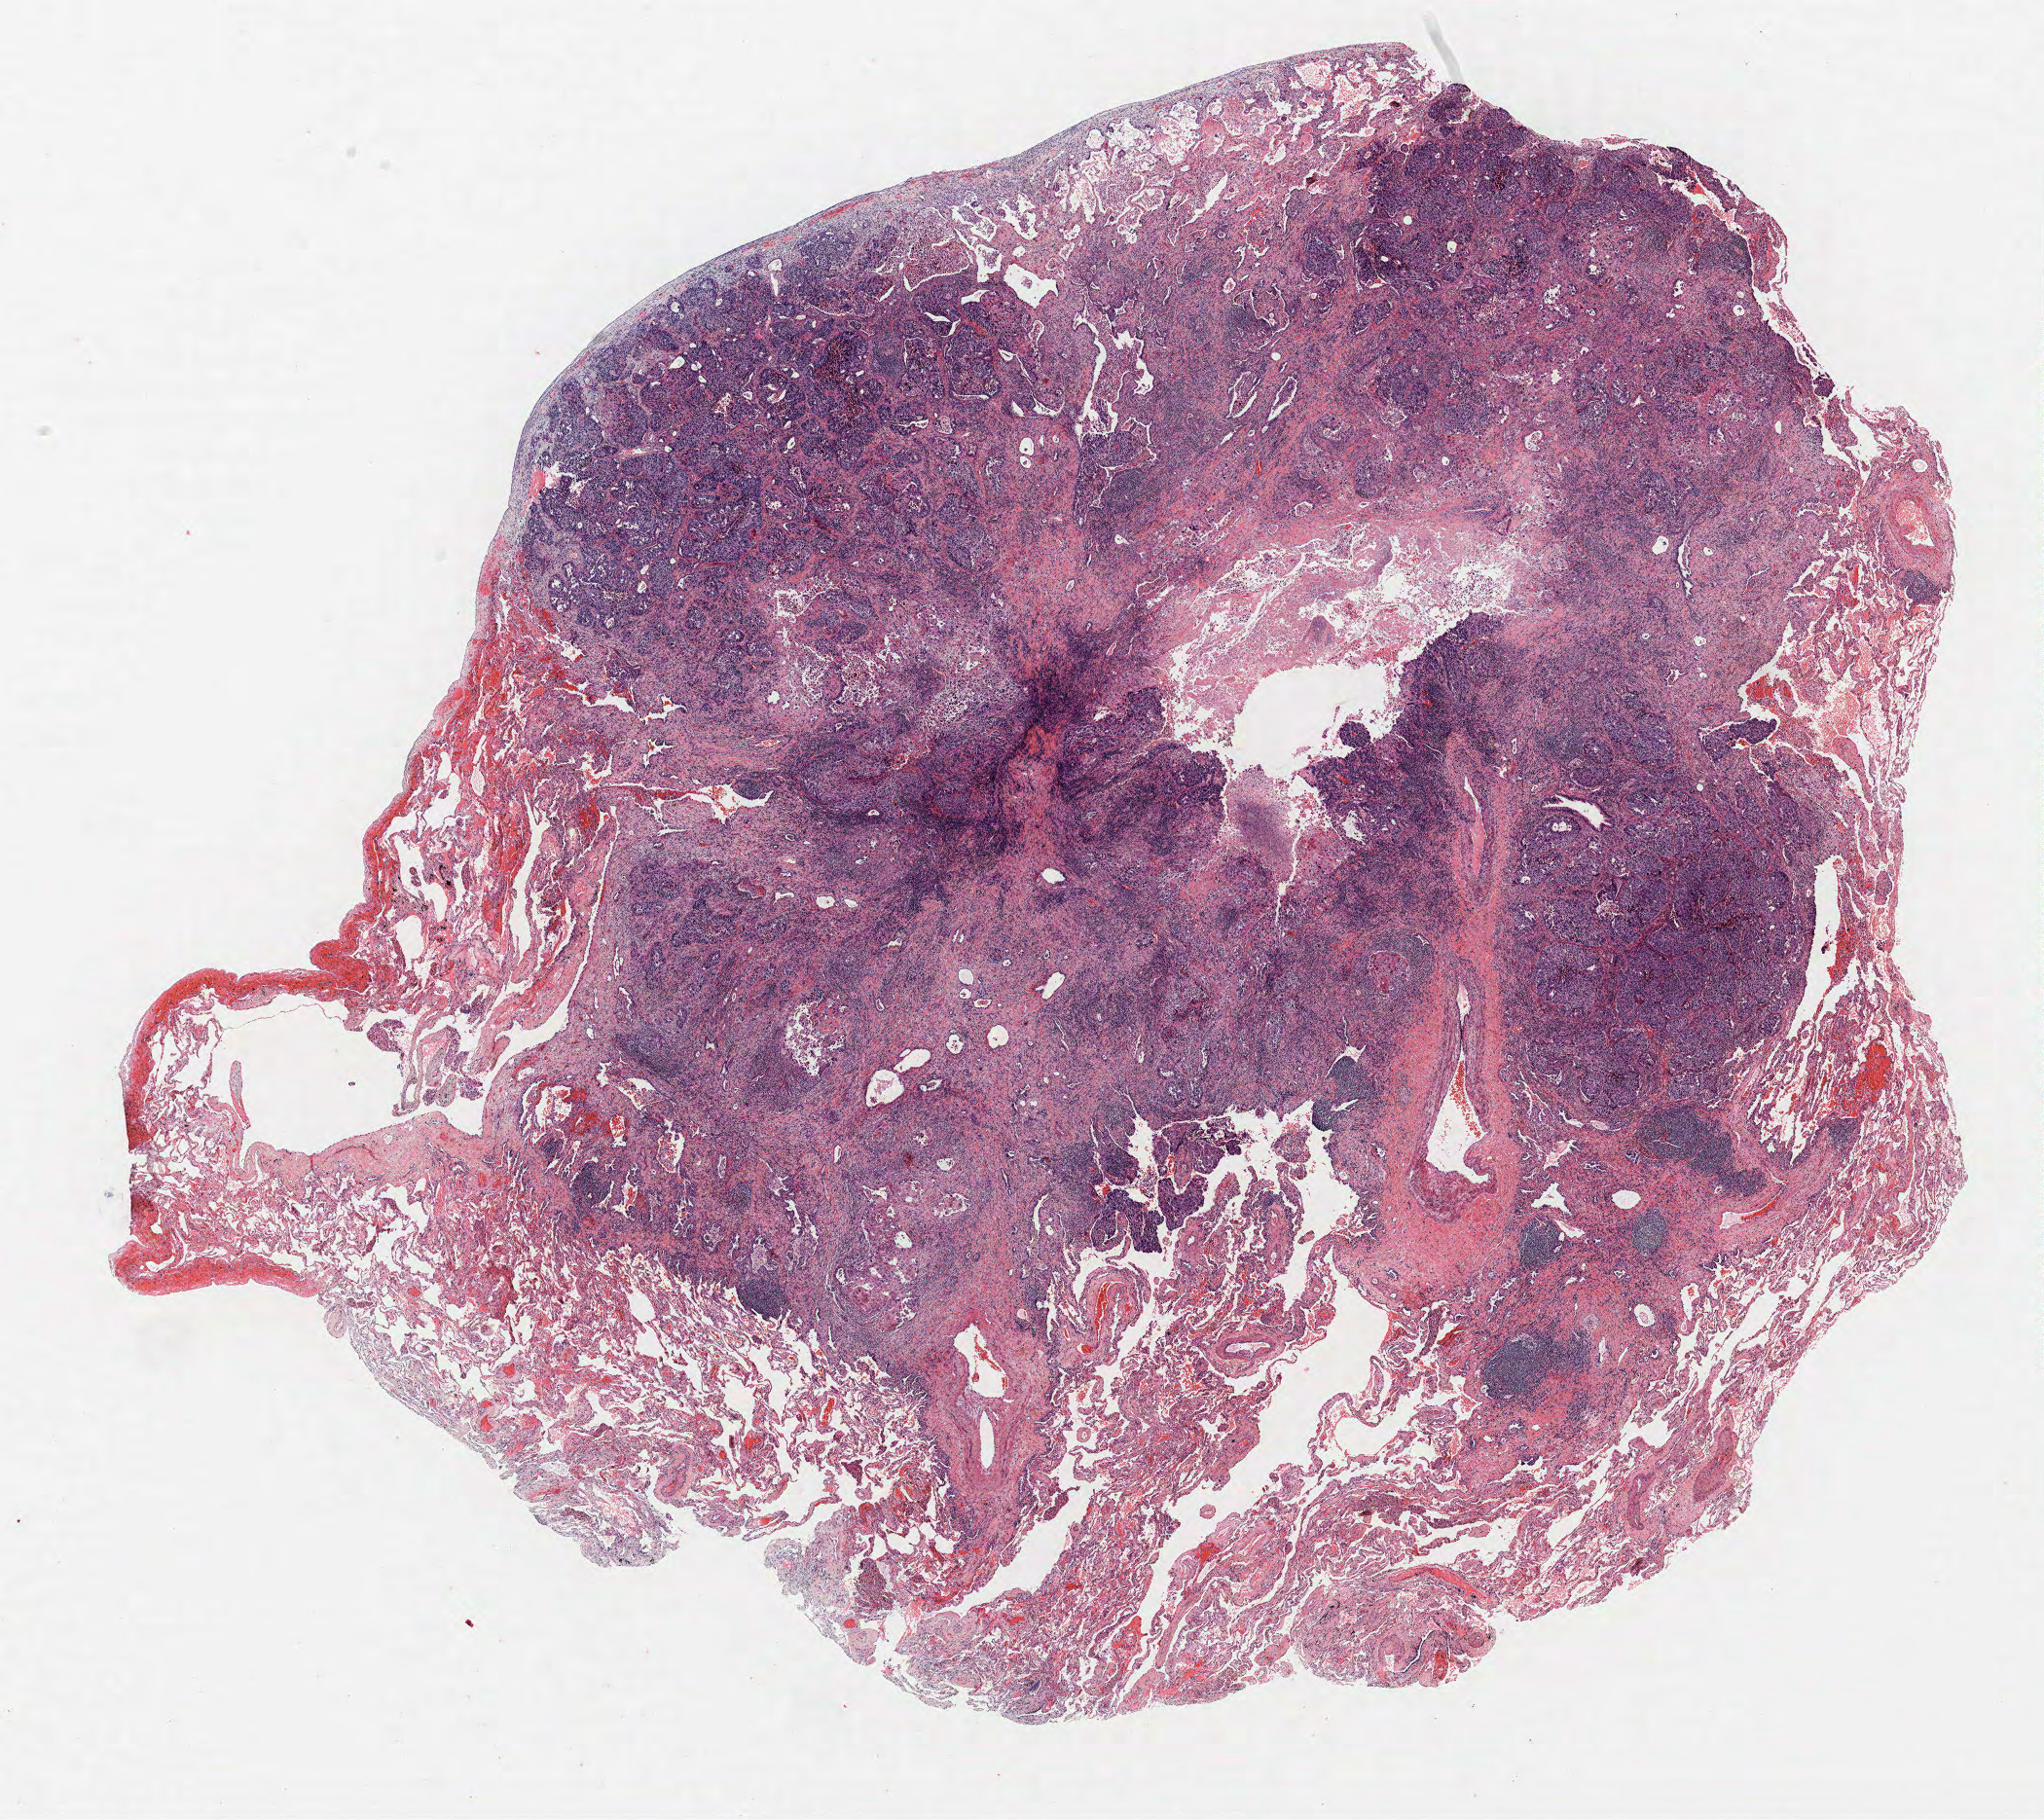
Whole-slide histology image, H&E-stained — shown as a low-resolution overview of the whole scanned area (about 16.8 x 15.0 mm); FFPE section; lung tissue. Female, age 63 at enrolment. Current smoker at enrolment.
Participant's lung-cancer diagnosis: Squamous cell carcinoma, NOS.